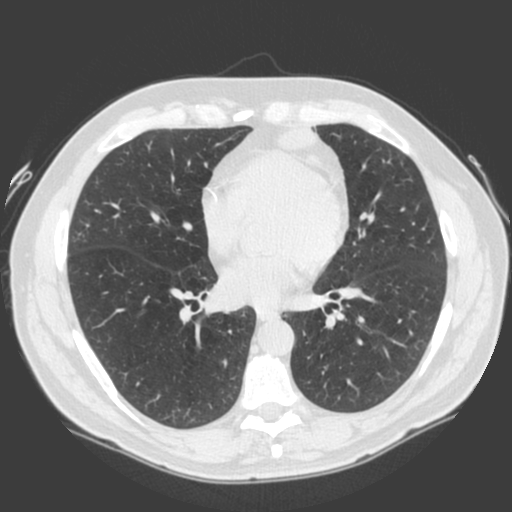
Low-dose screening chest CT, one axial slice; slice 86 of 185 in the series (ordered by position); 120 kVp; lung window (W 1500 / L -600 HU); 512 × 512 image matrix, field of view 360 × 360 mm.
Annotated regions visible in this slice (outlined manually by an expert reader):
- lesion 1 (tumor, lower lobe of left lung): bounding box [x1, y1, x2, y2] px = [277, 124, 342, 181]